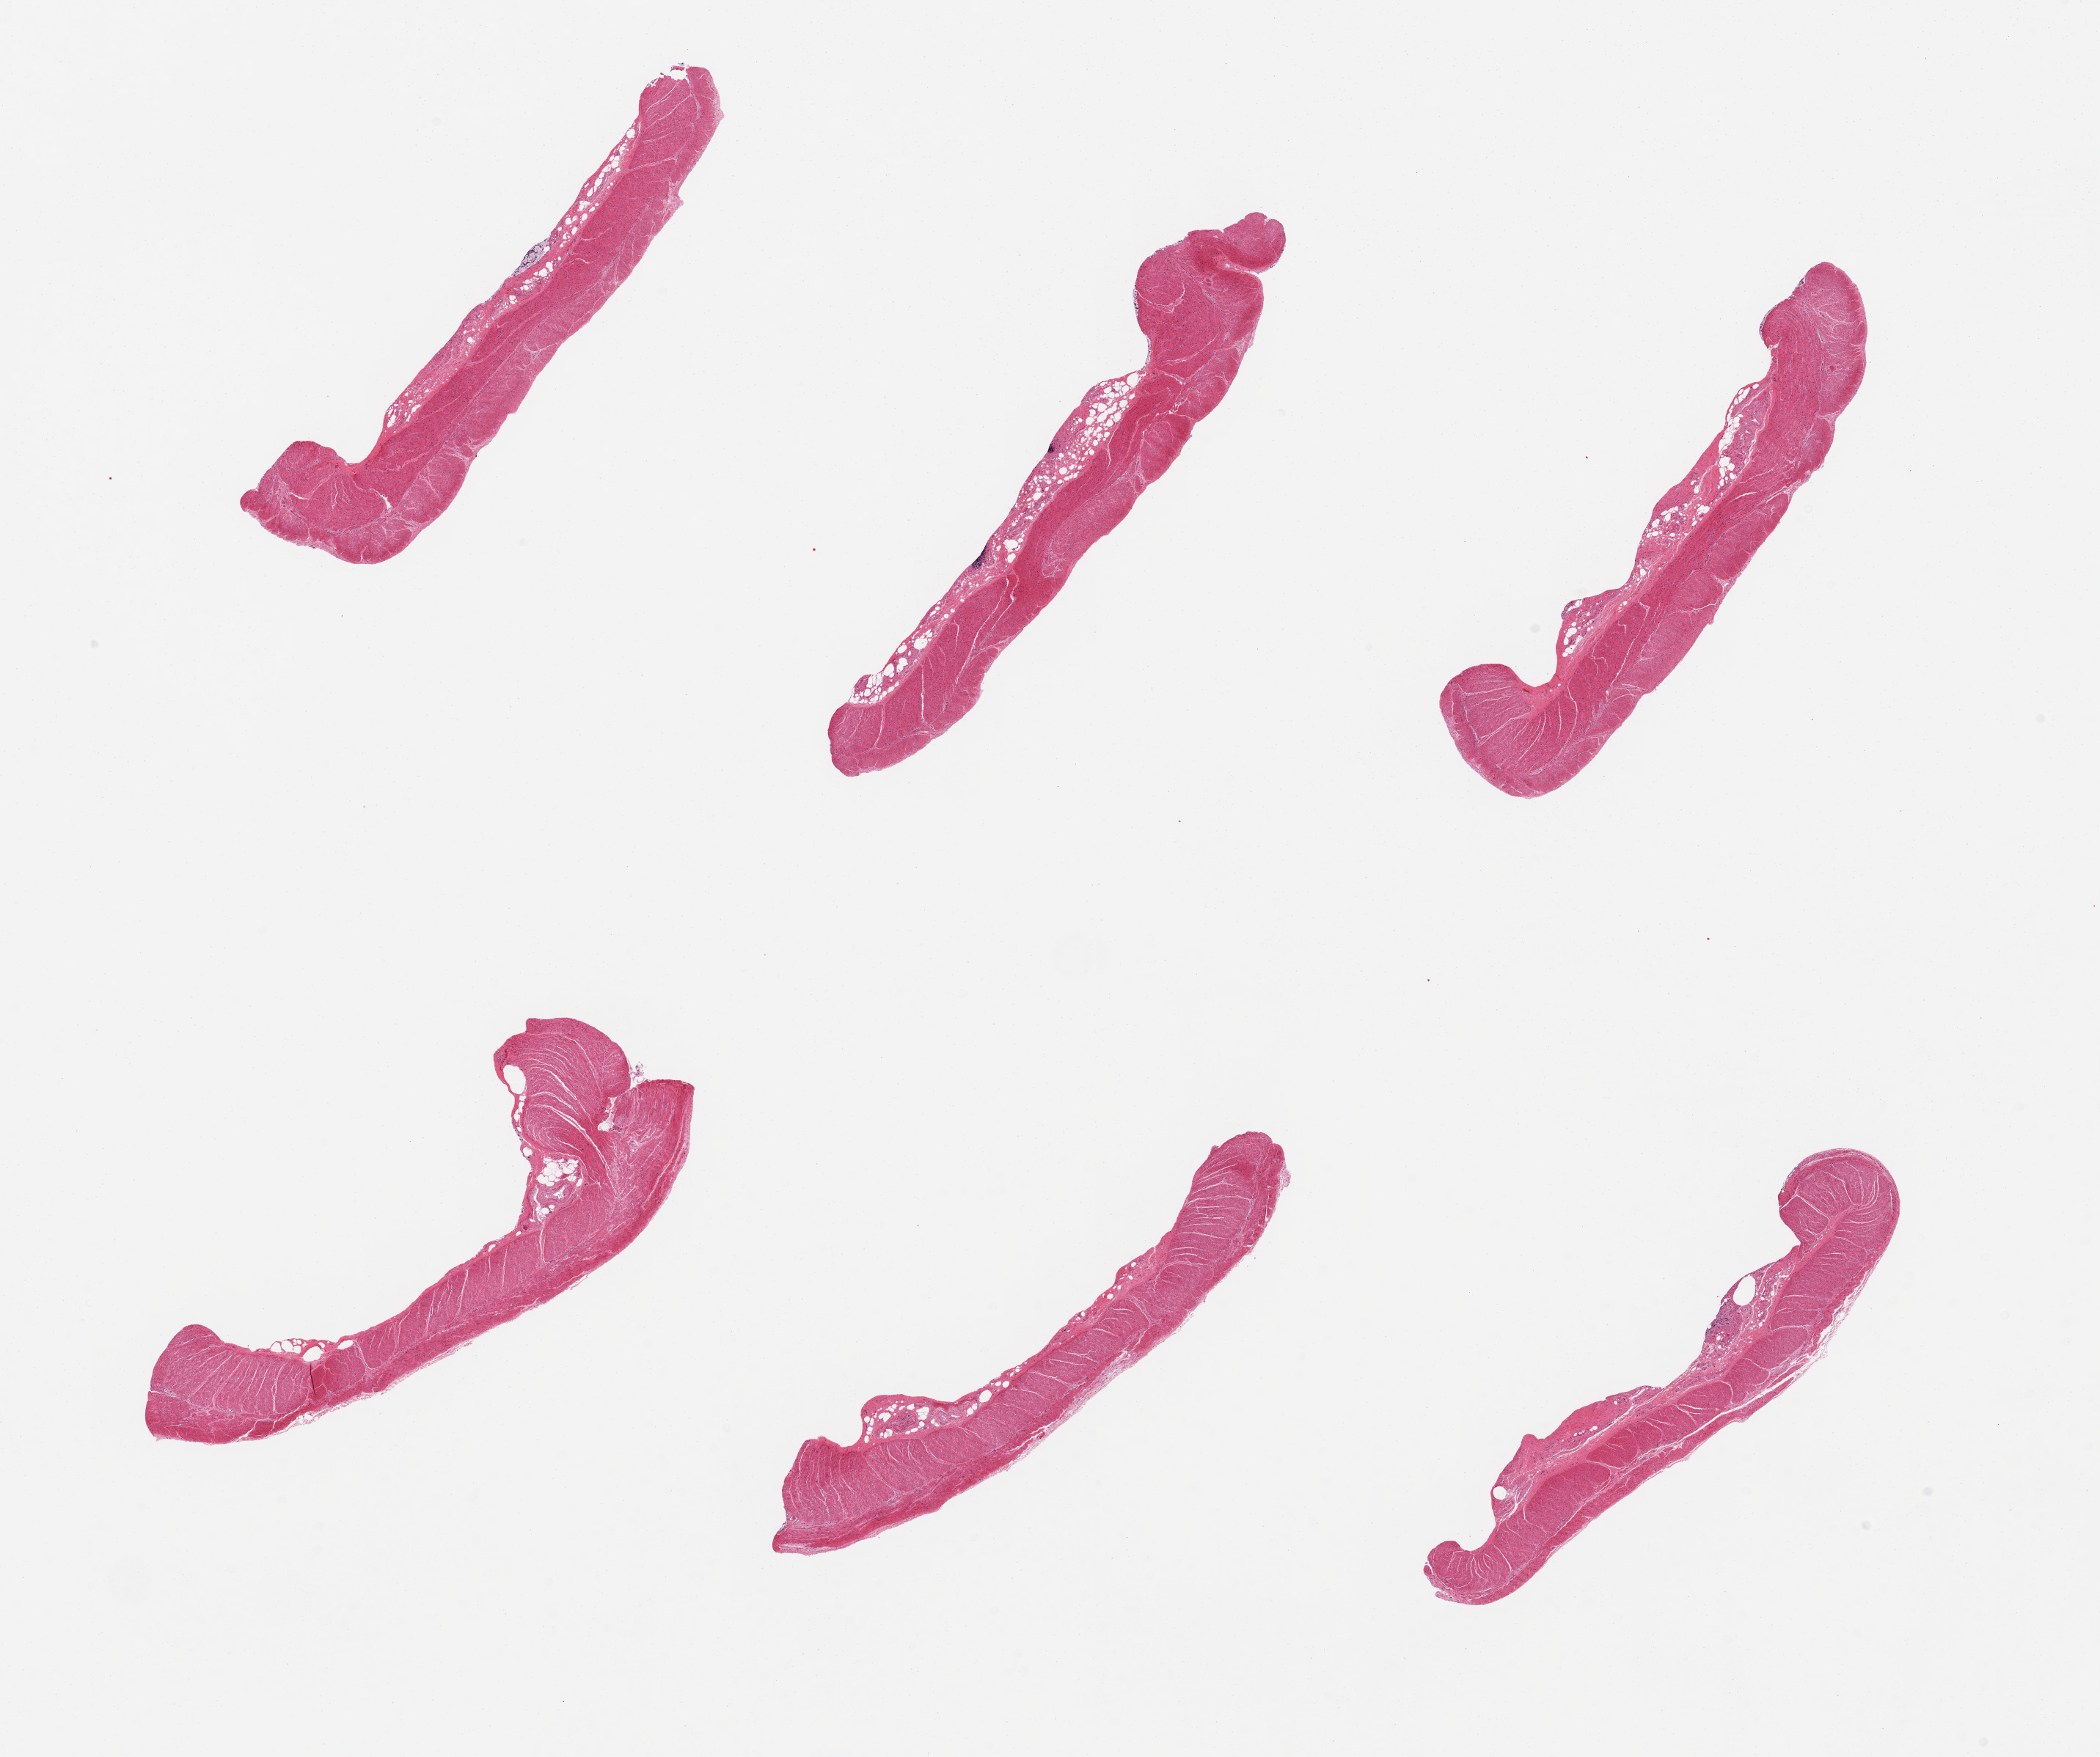
Hematoxylin and eosin (H&E) whole-slide image, brightfield — shown as a low-resolution overview of the whole scanned area (about 22.6 x 18.9 mm, acquisition: 20x scan). PAXgene-fixed, paraffin-embedded tissue. Target tissue: sigmoid colon. Donor tissue sample.
* pathologist's review note for this sample: 6 pieces, muscularis, small focus of autolyzed mucosa